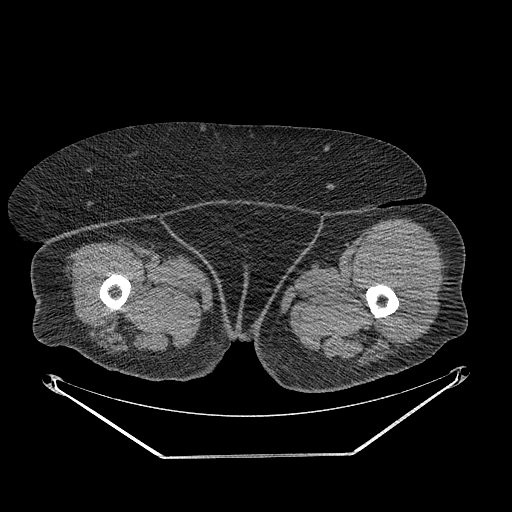
CT of an extremity soft-tissue mass (from a PET/CT study), one axial slice. Position 251 of 267 along the scan axis. Soft-tissue window (W 400 / L 40 HU). 3.75 mm slice thickness. 512 × 512 image matrix, field of view 500 × 500 mm. Female patient. Case-level facts recorded for this patient, not image findings: histological type: undifferentiated – high grade; grade: high; site of the primary tumour: left thigh.
Structures marked on this image (expert contour drawn on MRI and transferred to this co-registered scan by the dataset authors):
- gross tumour volume including surrounding oedema: box from (x=368, y=244) to (x=428, y=341) px
- gross tumour volume (mass): (x=370, y=246)–(x=426, y=337)